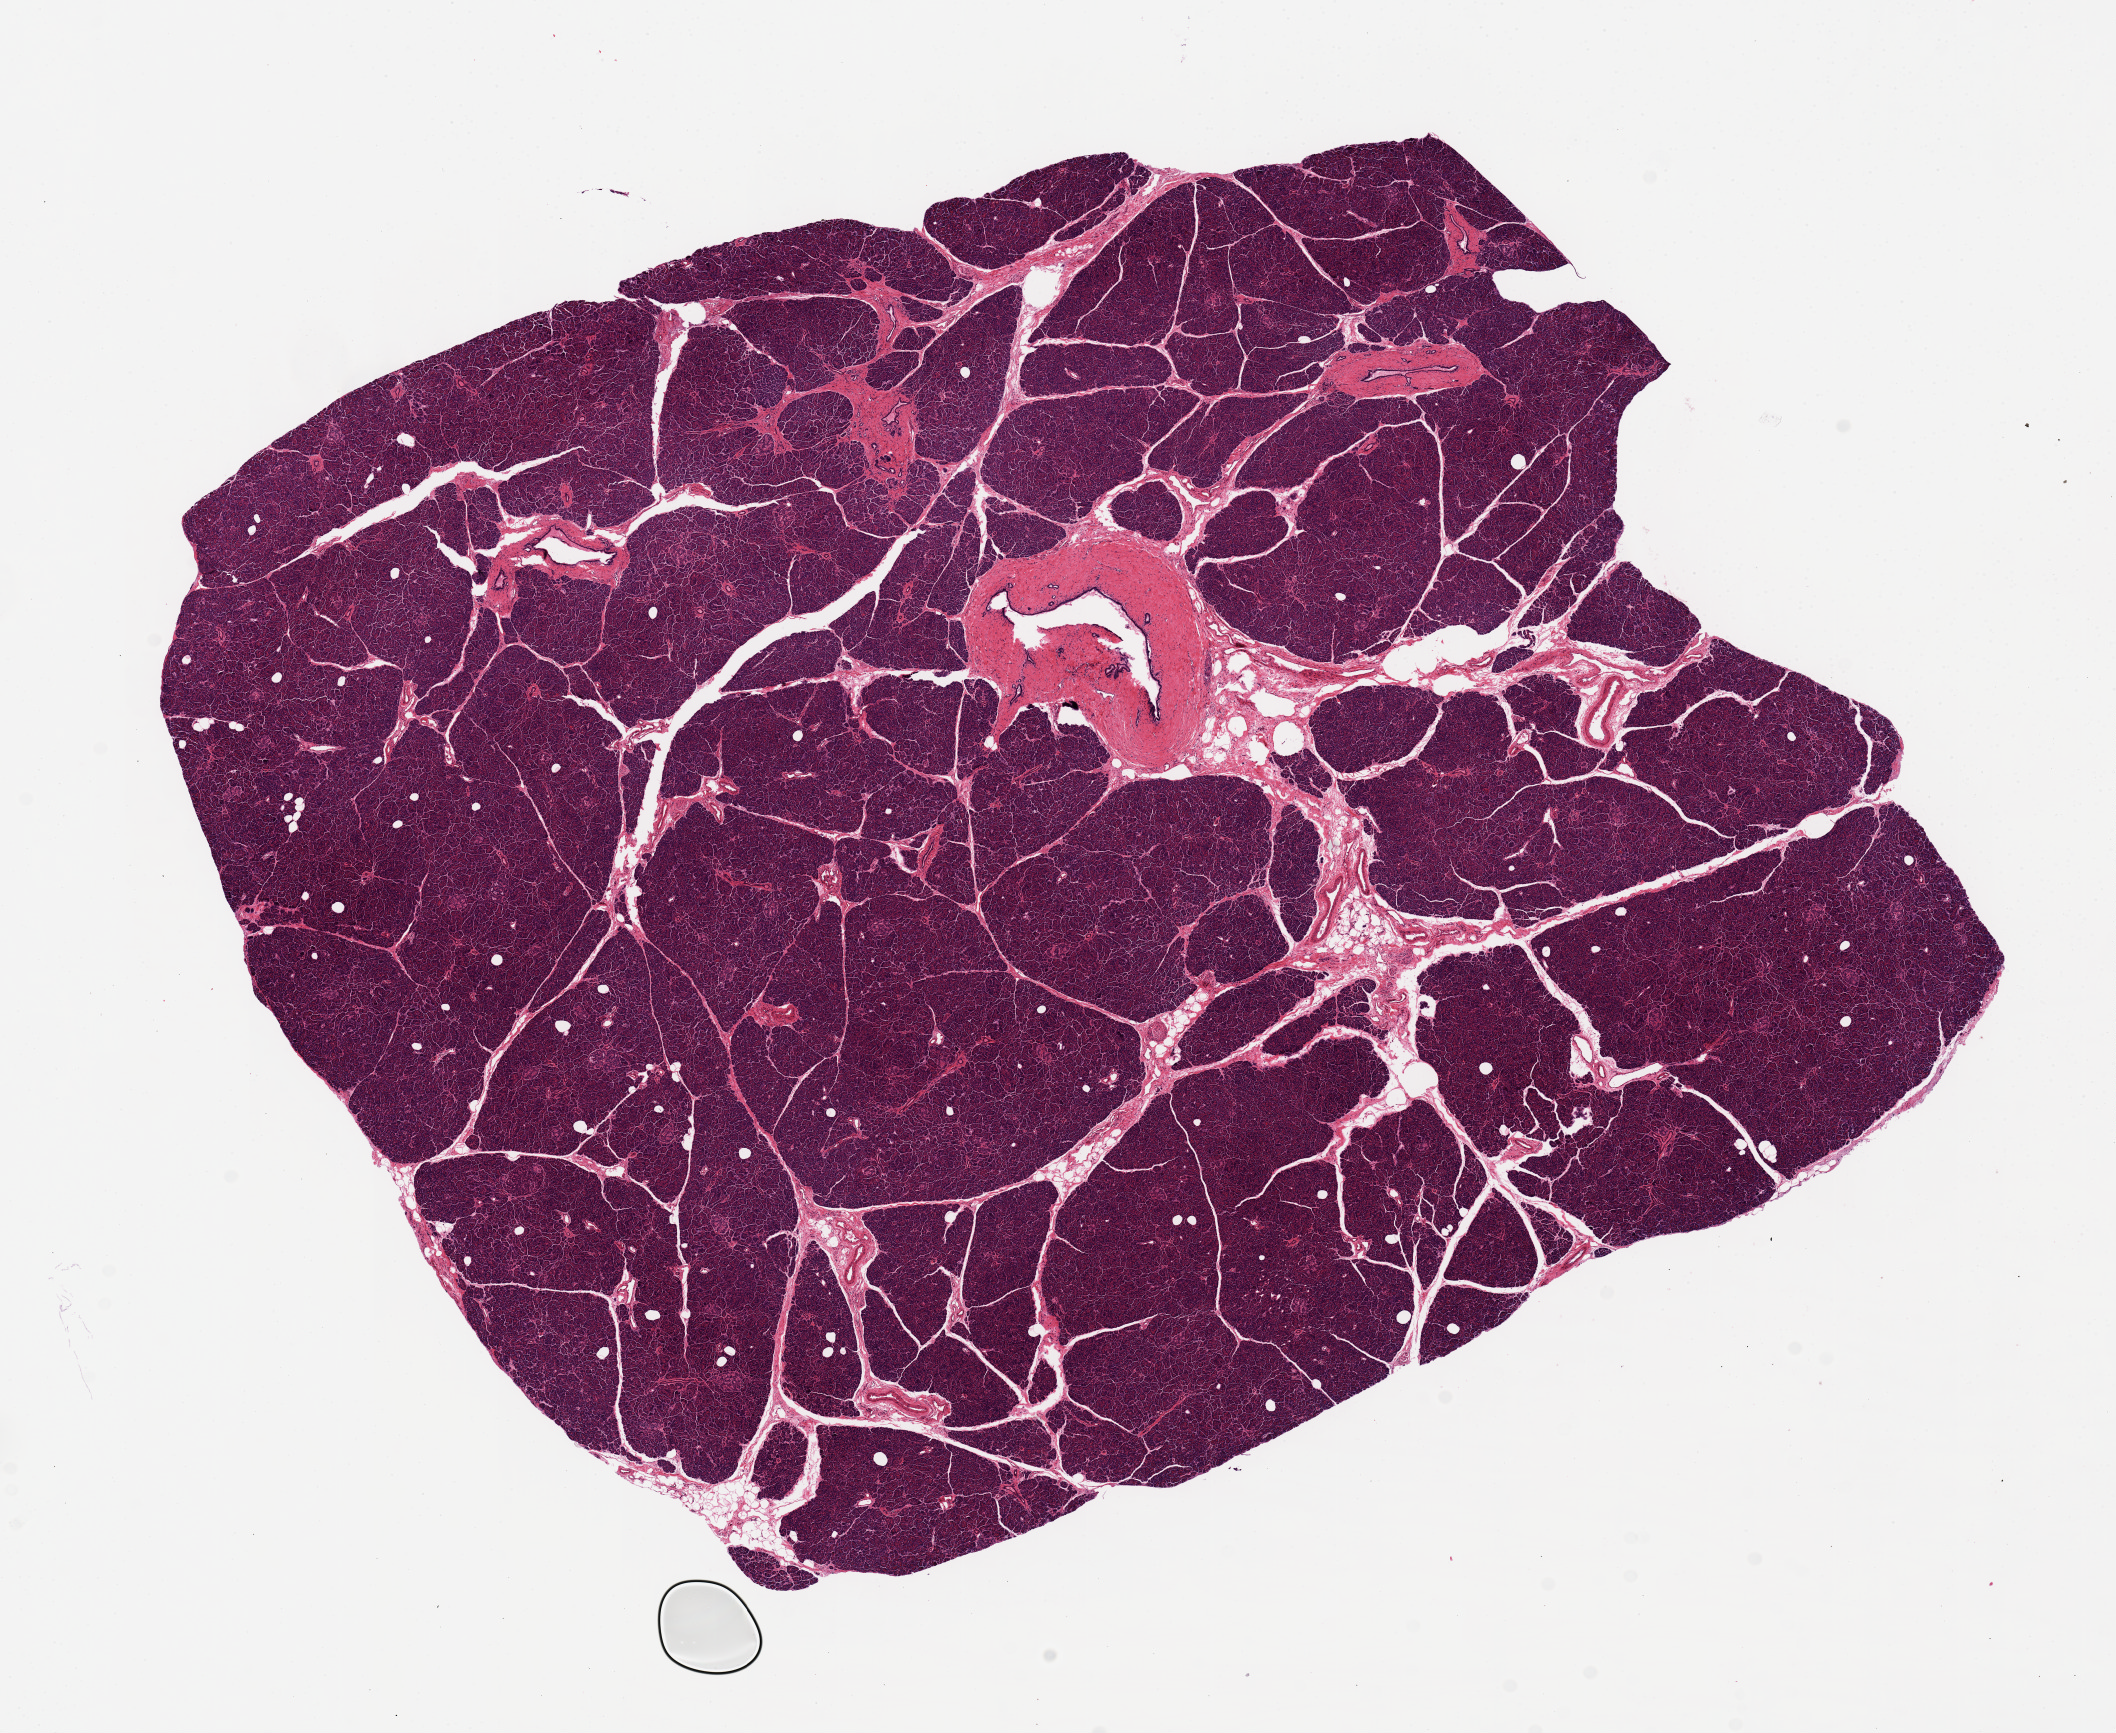
Whole-slide image, hematoxylin and eosin (H&E) stain, whole scanned area (about 16.7 x 13.7 mm, acquisition: 20x scan) shown as a low-resolution overview, PAXgene-fixed paraffin-embedded (PFPE) section, target tissue: pancreas, donor tissue sample. Donor sex: male.
Reviewer comment on this tissue sample: 1. 11.5x10.4mm. Remarkably well-preserved.